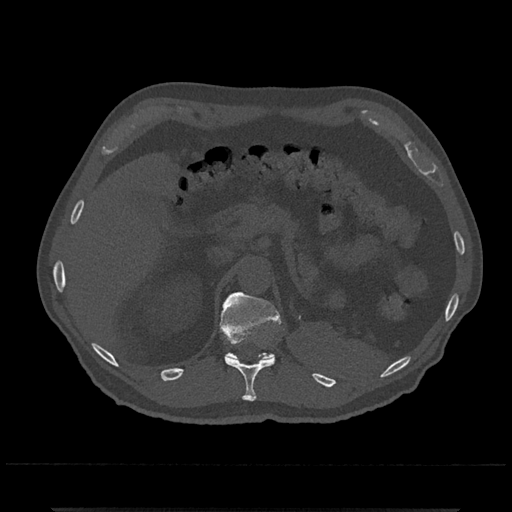
CT including the spine, one axial slice. Slice 465 of 797 in the series (ordered by position). Reconstruction kernel Br40s/3. 120 kVp. Bone window (W 1800 / L 400 HU). 0.5 mm slice thickness. 512 × 512 image matrix, field of view 393 × 393 mm. Patient: male, 67 years. From the clinical record (not read from this slice): primary cancer: prostate.
Structures marked on this image (semi-automatic segmentation, software-assisted and operator-edited):
- T11 vertebra: box from (x=225, y=335) to (x=276, y=401) px
- T12 vertebra: (x=220, y=292)–(x=282, y=360)